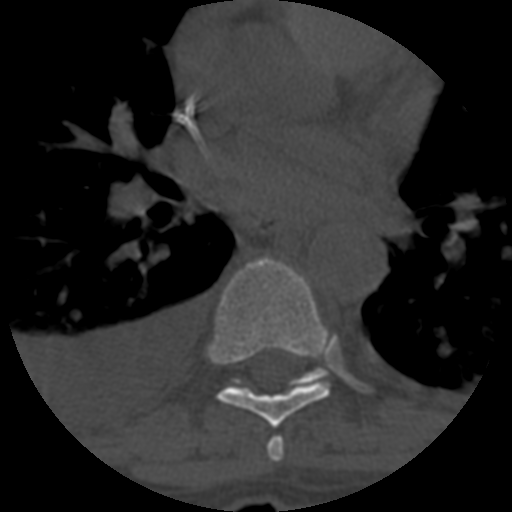
CT including the spine, one axial slice. Slice 413 of 708 in the series (ordered by position). Reconstruction kernel STANDARD. 120 kVp. One of 3 acquisitions stored at this slice position. Bone window (W 1800 / L 400 HU). 1.25 mm slice thickness. 512 × 512 image matrix, field of view 160 × 160 mm. Patient age 55 years. Case-level facts recorded for this patient, not image findings: primary cancer: colon.
Annotated regions visible in this slice (semi-automatic segmentation, software-assisted and operator-edited):
- T6 vertebra: box from (x=267, y=437) to (x=284, y=462) px
- T7 vertebra: (x=209, y=257)–(x=331, y=428)
- T8 vertebra: (x=234, y=368)–(x=327, y=383)